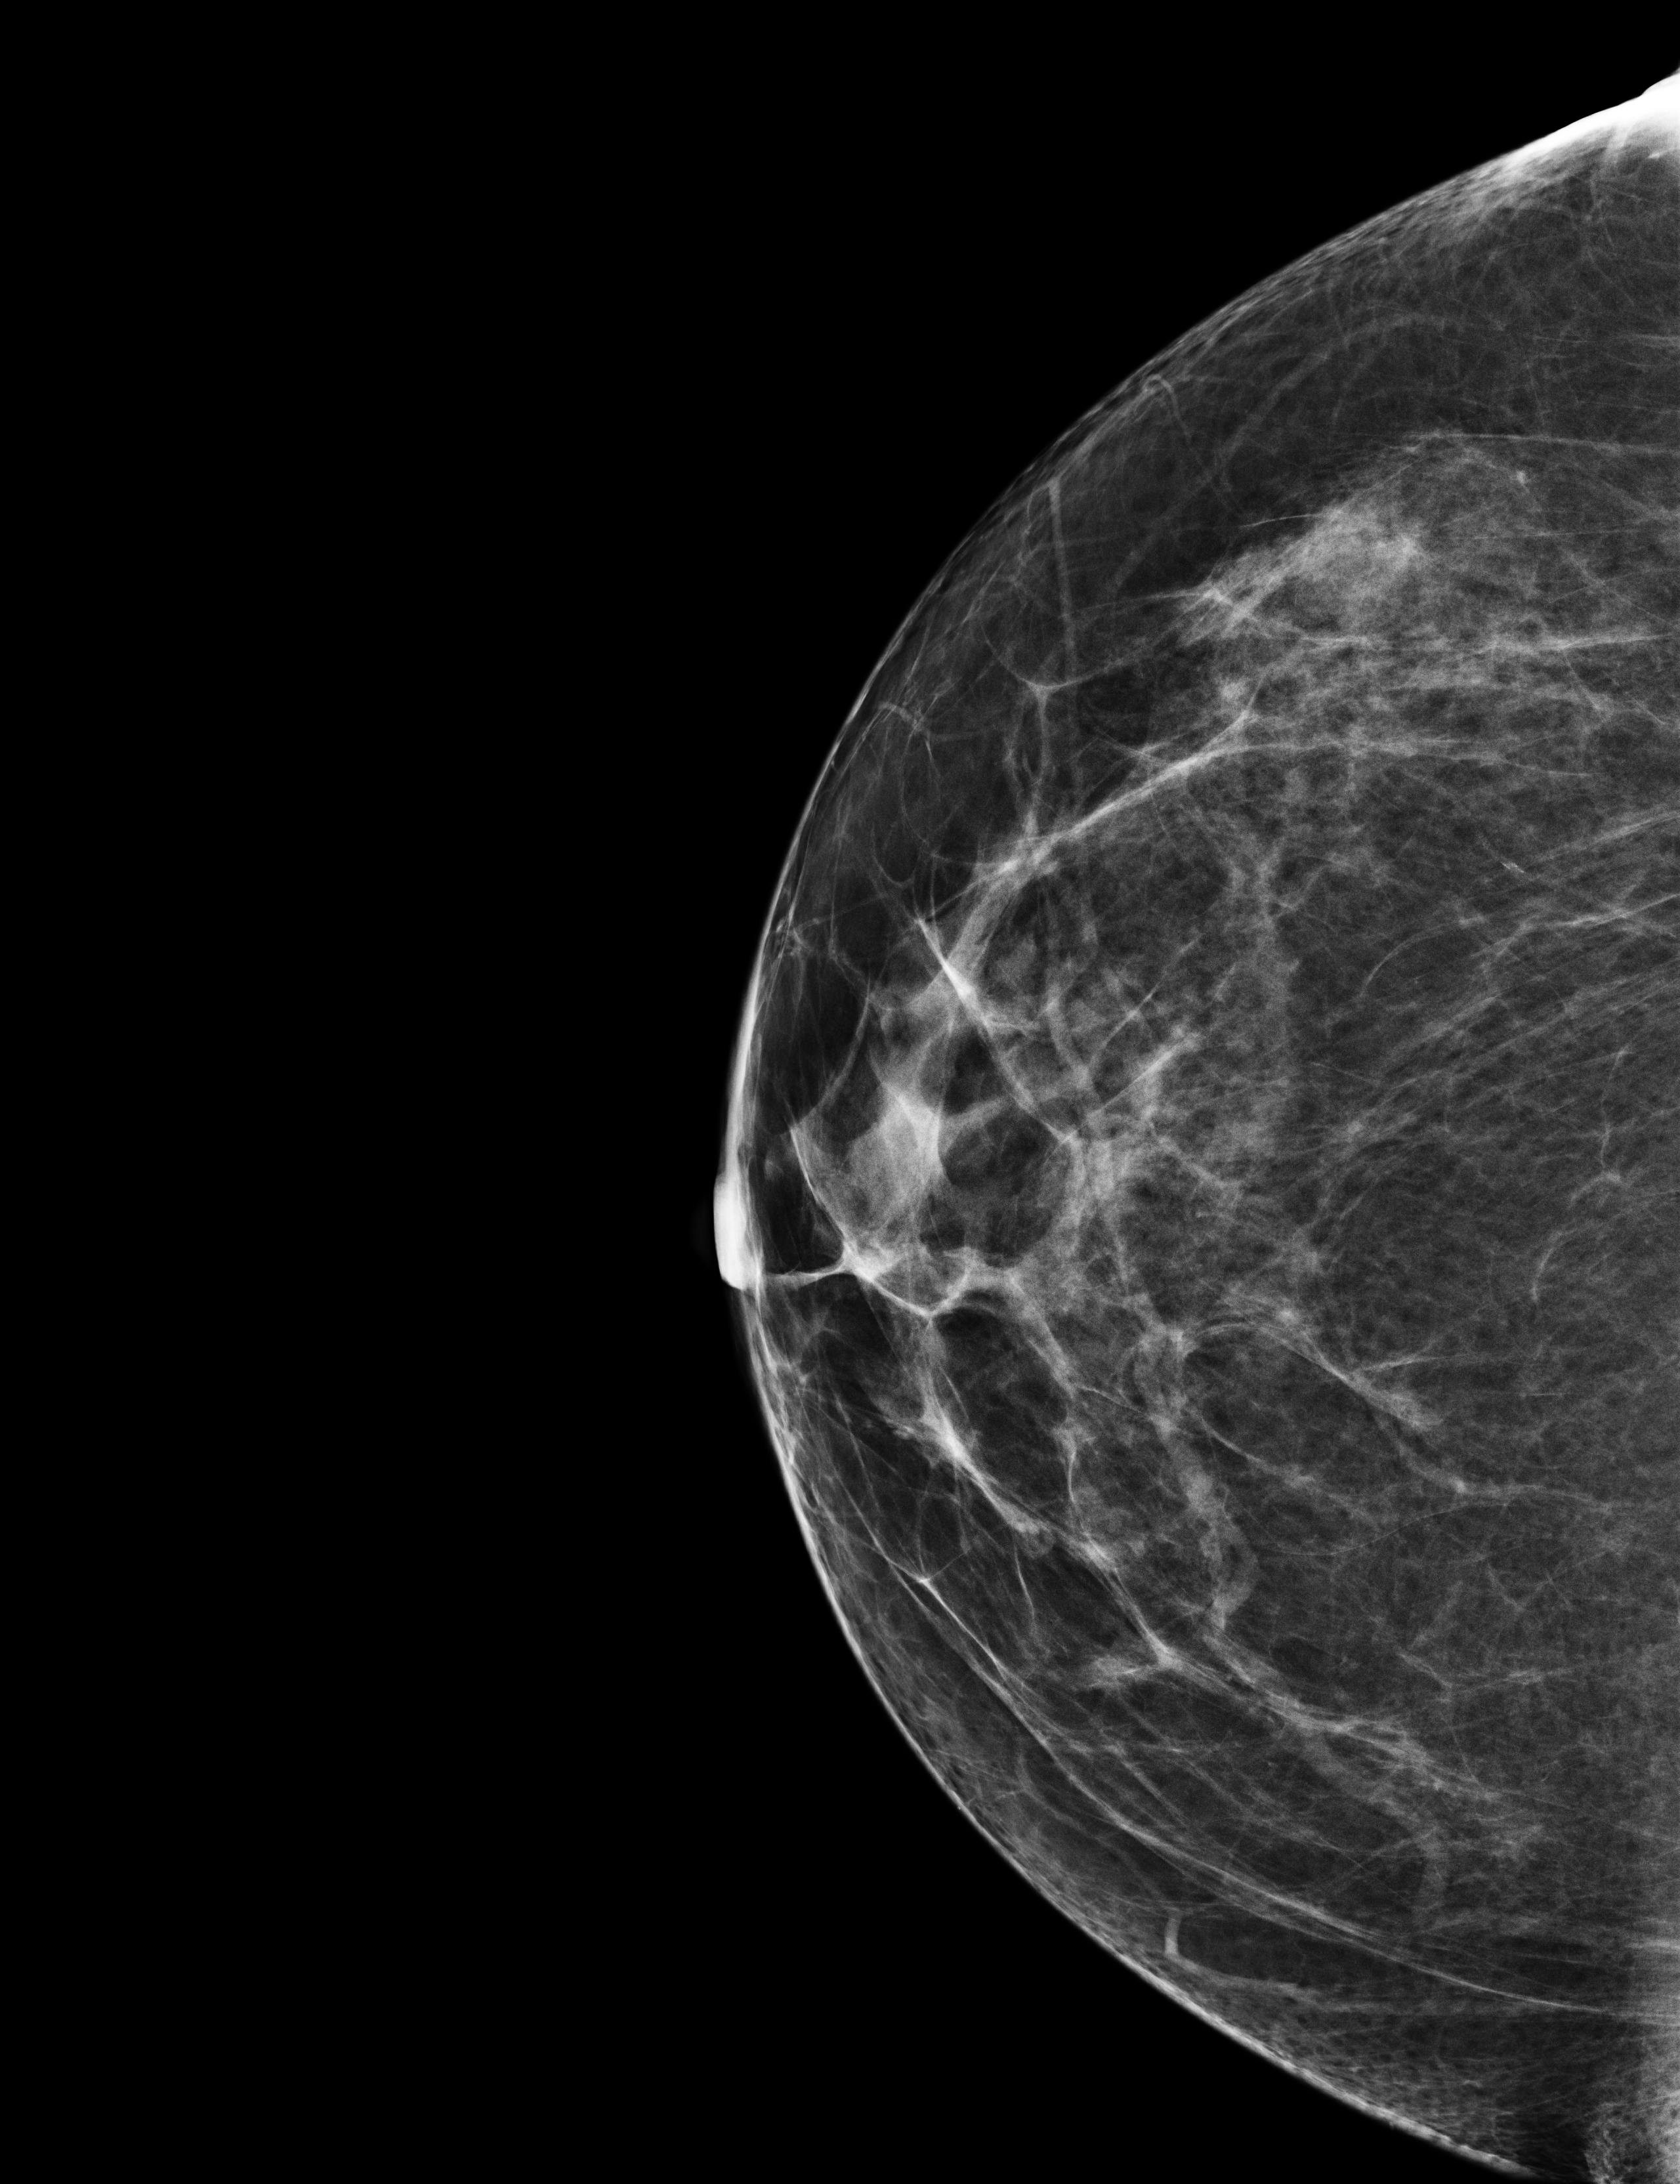
Screening examination, compressed breast thickness 72 mm, system: Selenia Dimensions. Female patient, age 57 years.
Image type: full-field digital mammogram. Breast: right. Projection: craniocaudal (CC) view.